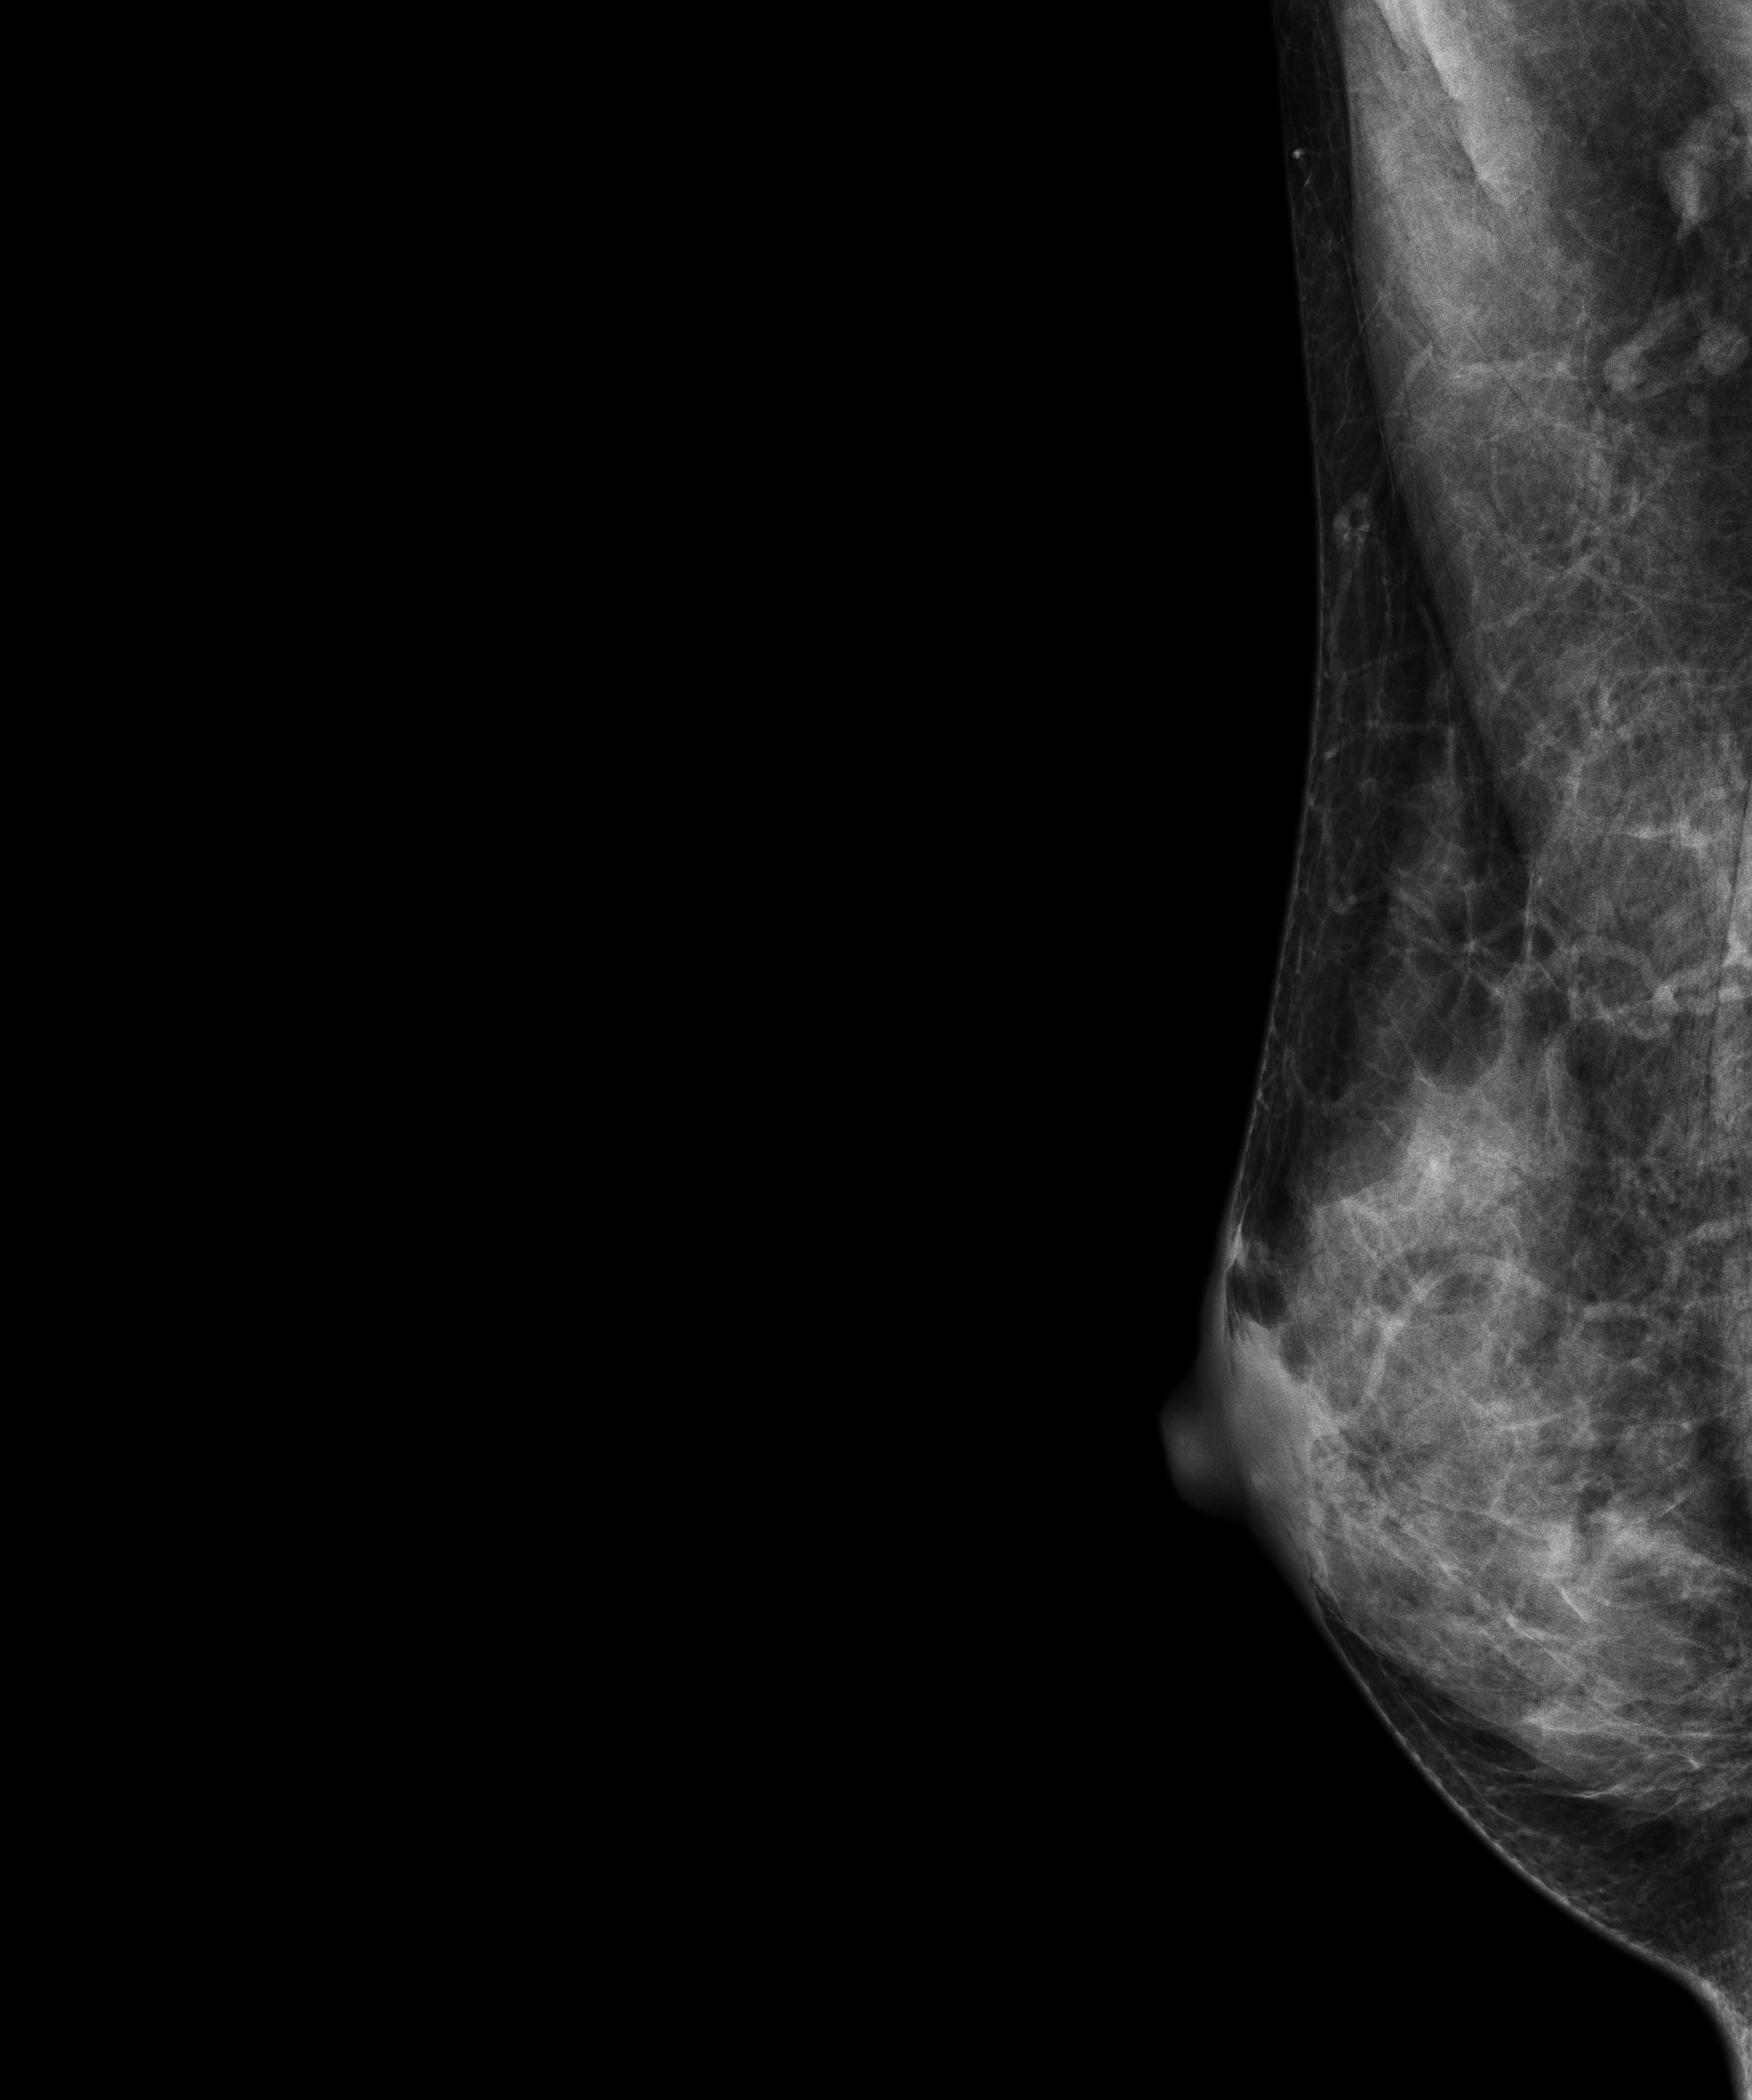
Digital mammogram (FFDM); right breast; MLO view; annual screening mammography examination; compressed breast thickness 39 mm; system: Senographe Essential ADS_56.21.3. Patient: female, 46 years.
Breast density at the screening exam (both breasts): extremely dense (BI-RADS density category d). Final BI-RADS category for the screening round (tomosynthesis exam, both breasts): category 1. Recall: no recall after this screen.